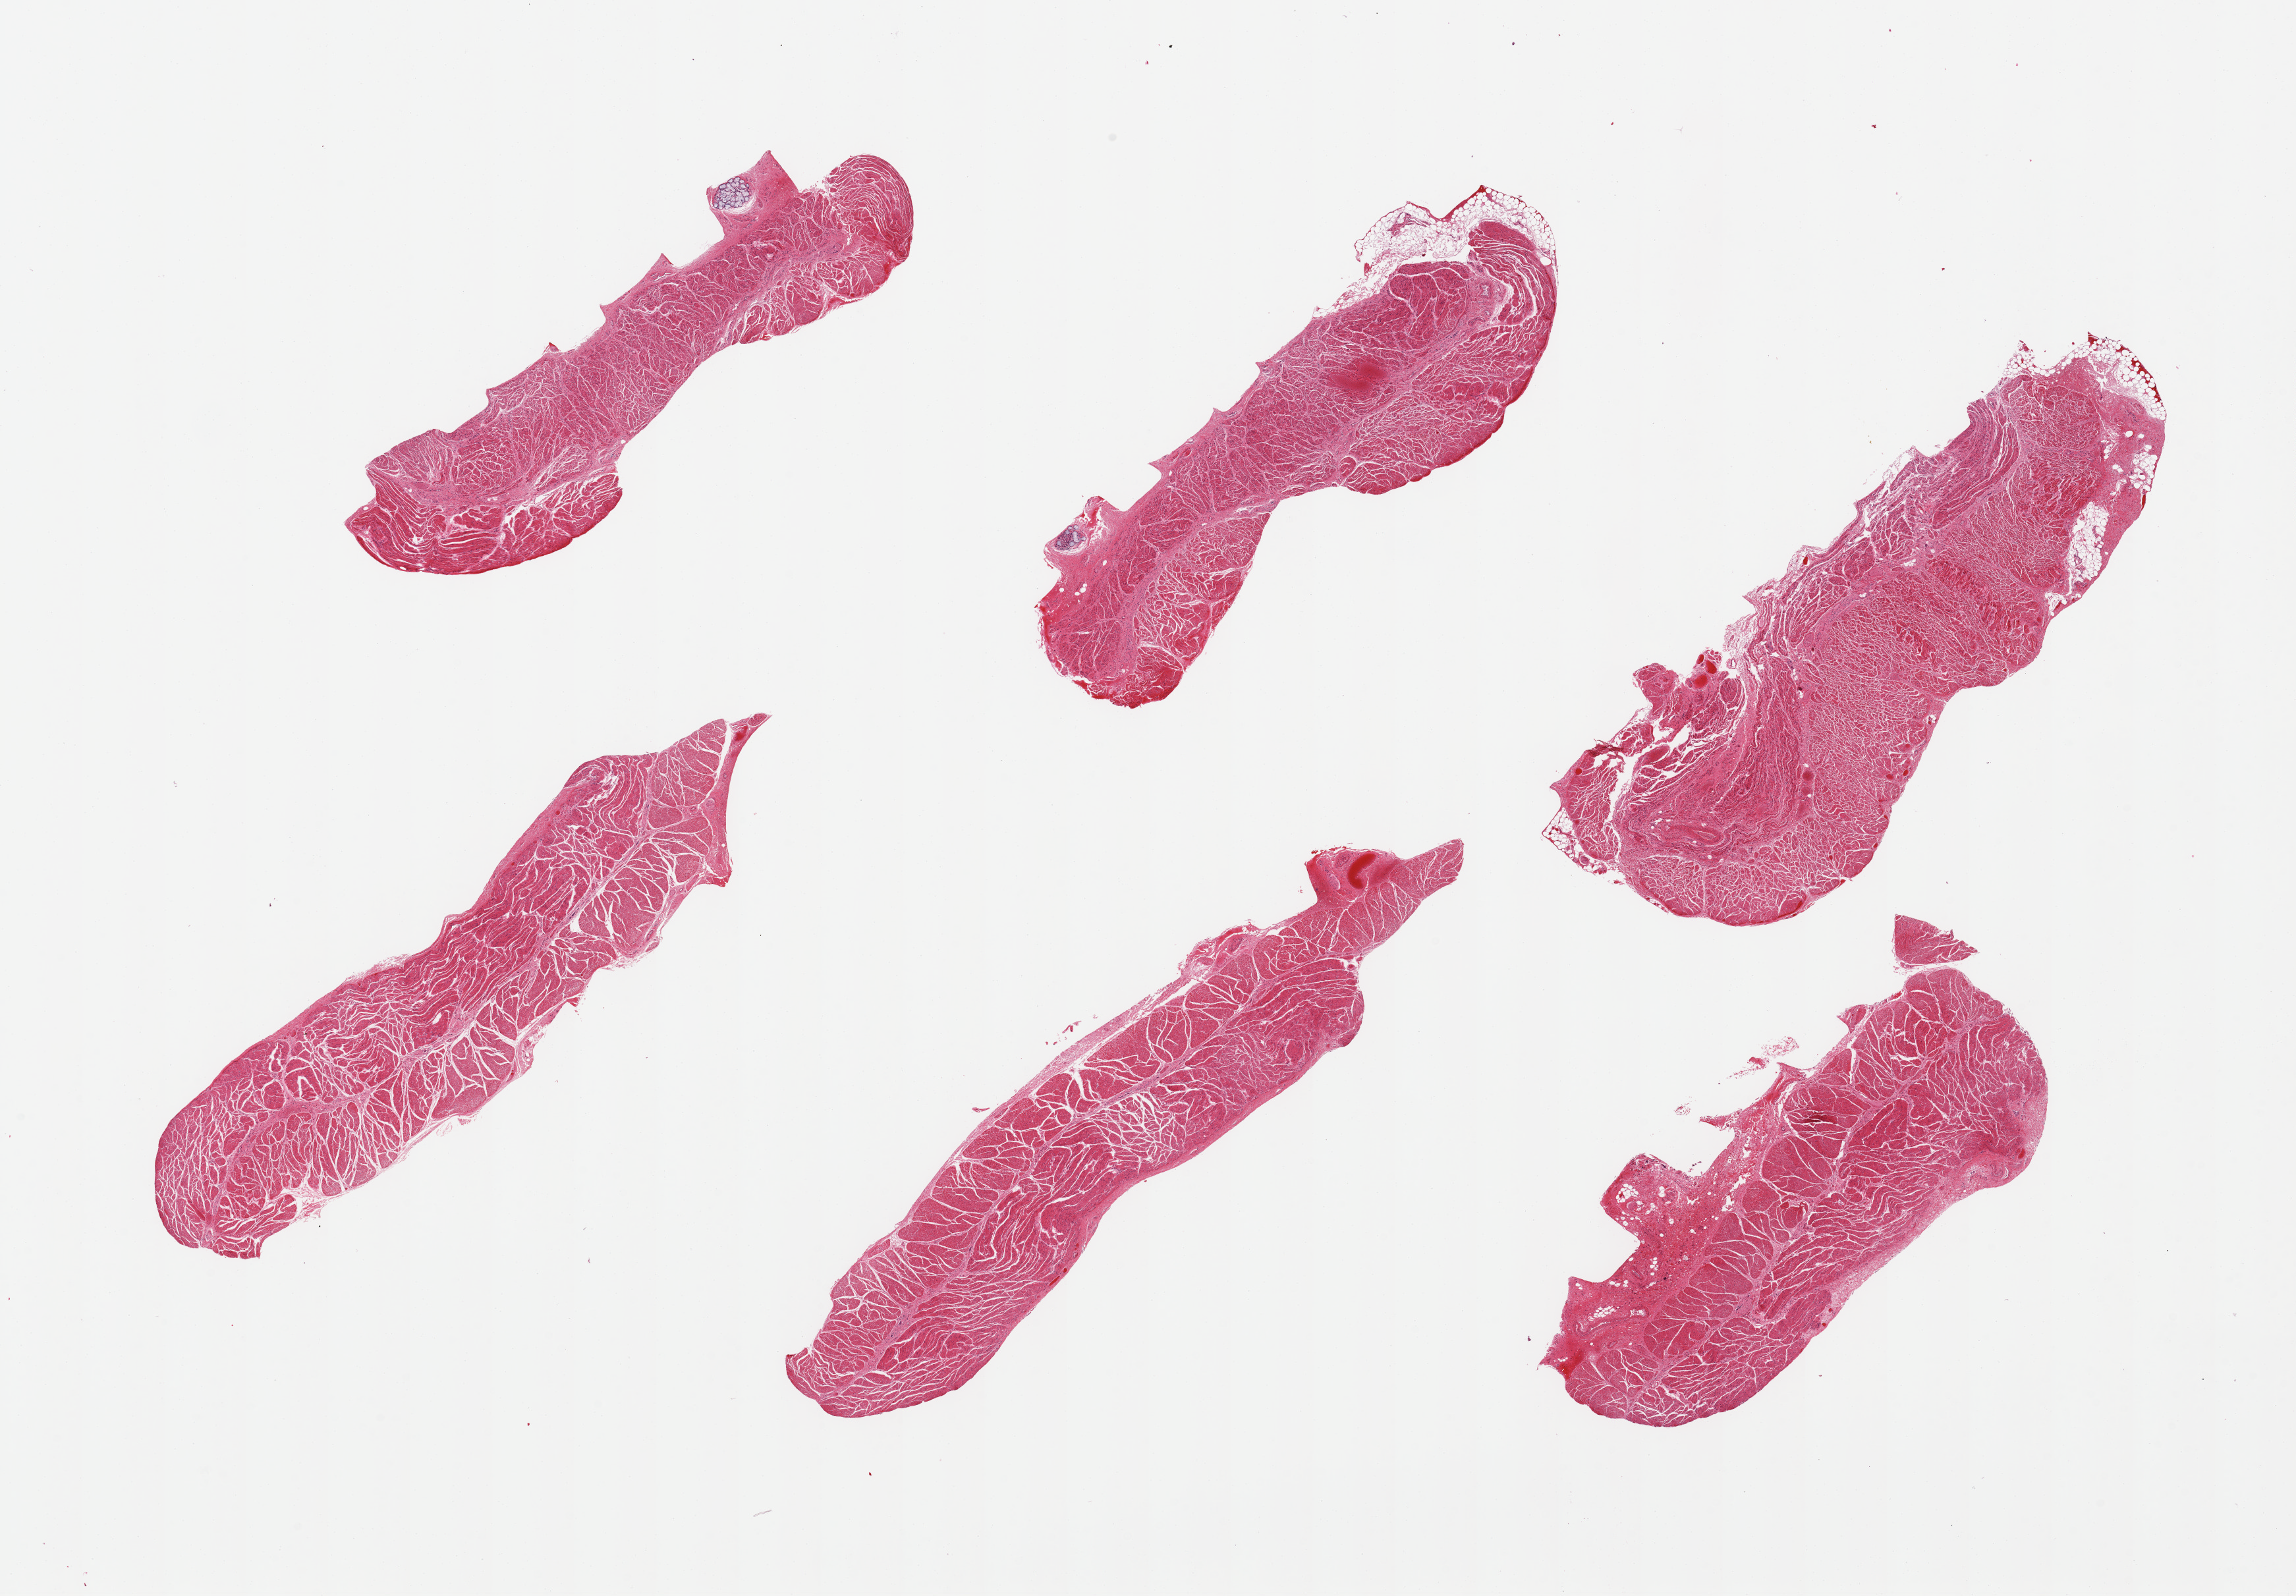
Digitized H&E-stained section — low-resolution overview of the scanned area, about 27.6 x 19.2 mm. PAXgene-fixed, paraffin-embedded tissue. Section of gastroesophageal junction (target tissue). Donor tissue sample. Donor: male.
Reviewer comment on this tissue sample: 6 pieces; 2 pieces have small submucosal gland remnants.